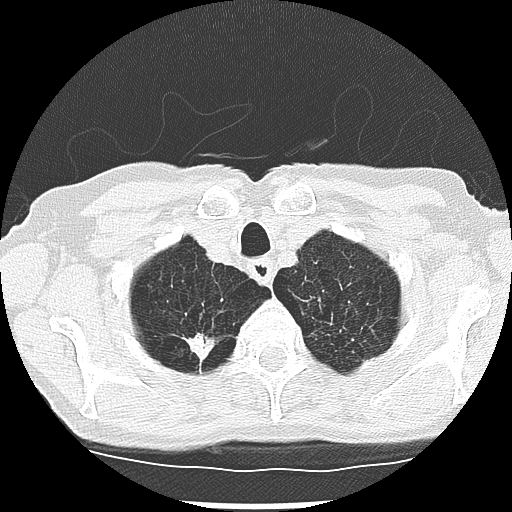
Low-dose screening chest CT, one axial slice. Slice 240 of 265 in the series (ordered by position). Reconstruction kernel LUNG. Lung window (W 1500 / L -600 HU). 512 × 512 image matrix, field of view 300 × 300 mm.
Structures marked on this image (manually delineated by an expert):
- lesion 2 (tumor, upper lobe of right lung): box from (x=186, y=333) to (x=215, y=361) px